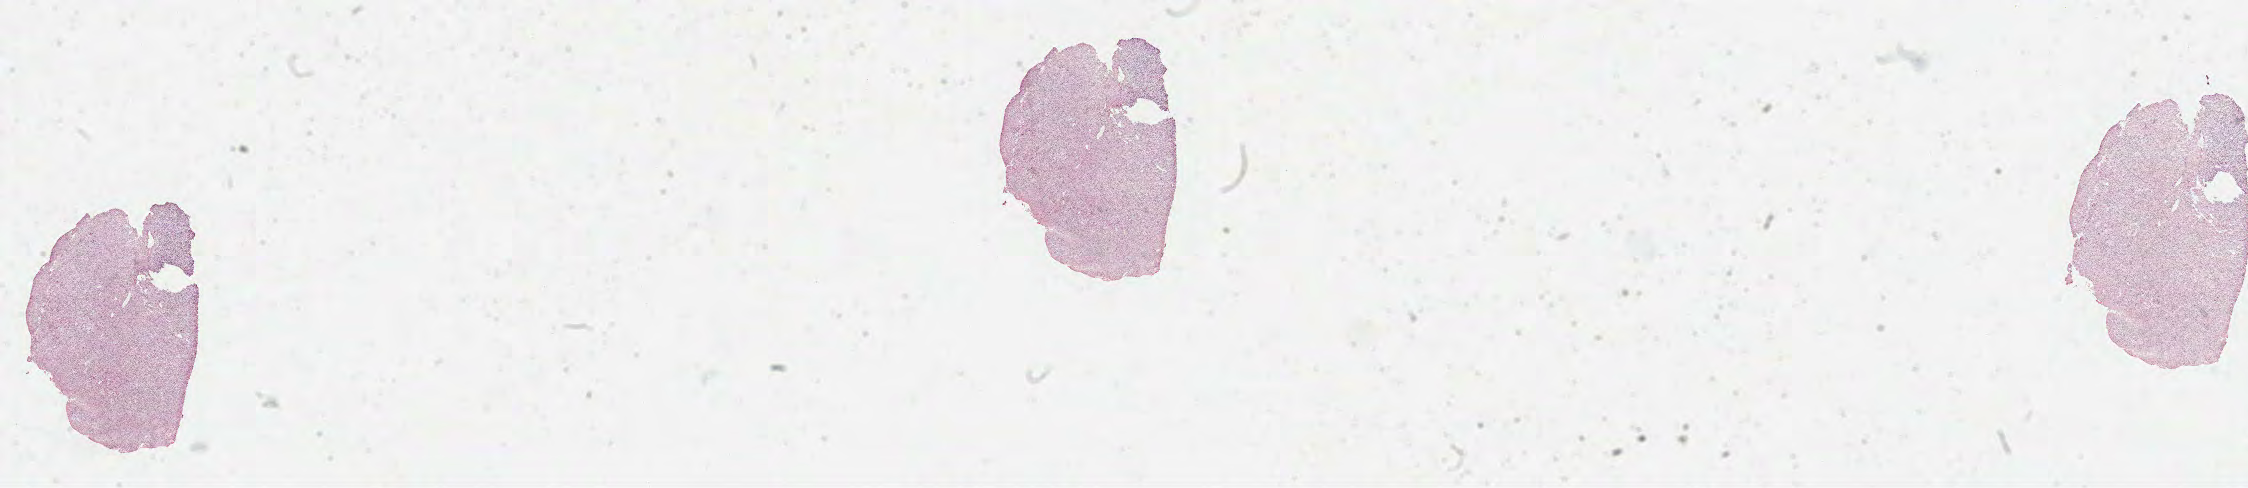
Whole-slide histology image, H&E — low-resolution overview of the scanned area, about 36.3 x 7.9 mm (from a 40x scan). Formalin-fixed paraffin-embedded (FFPE) diagnostic section. Primary tumour sample from the brain. Male patient; age at initial diagnosis 65 years.
* pathologic diagnosis: Glioblastoma